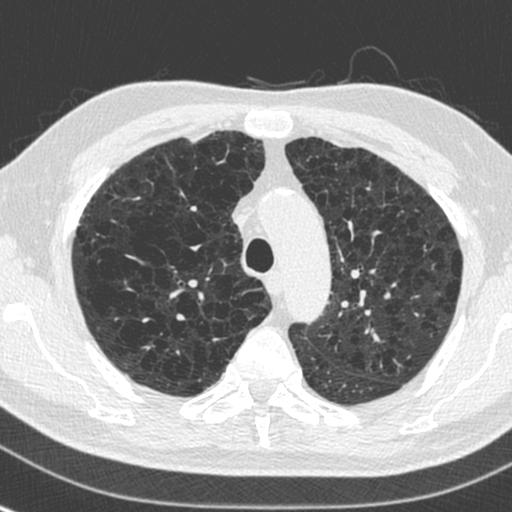
Axial slice from a low-dose chest CT screening exam; baseline annual screen; lung window (W 1500 / L -600 HU); 1.3 mm slice thickness. Male, age 73 years at enrolment.
Expert reader's lesion annotation, bounding box <153,250,199,287> (left, top, right, bottom; pixels). No non-calcified nodule or mass ≥4 mm was recorded by the screening reader at this exam. Later outcome: lung cancer diagnosed 446 days after this screen — squamous cell carcinoma, NOS, right upper lobe, stage IA (AJCC 6th edition), 10 mm at pathology.